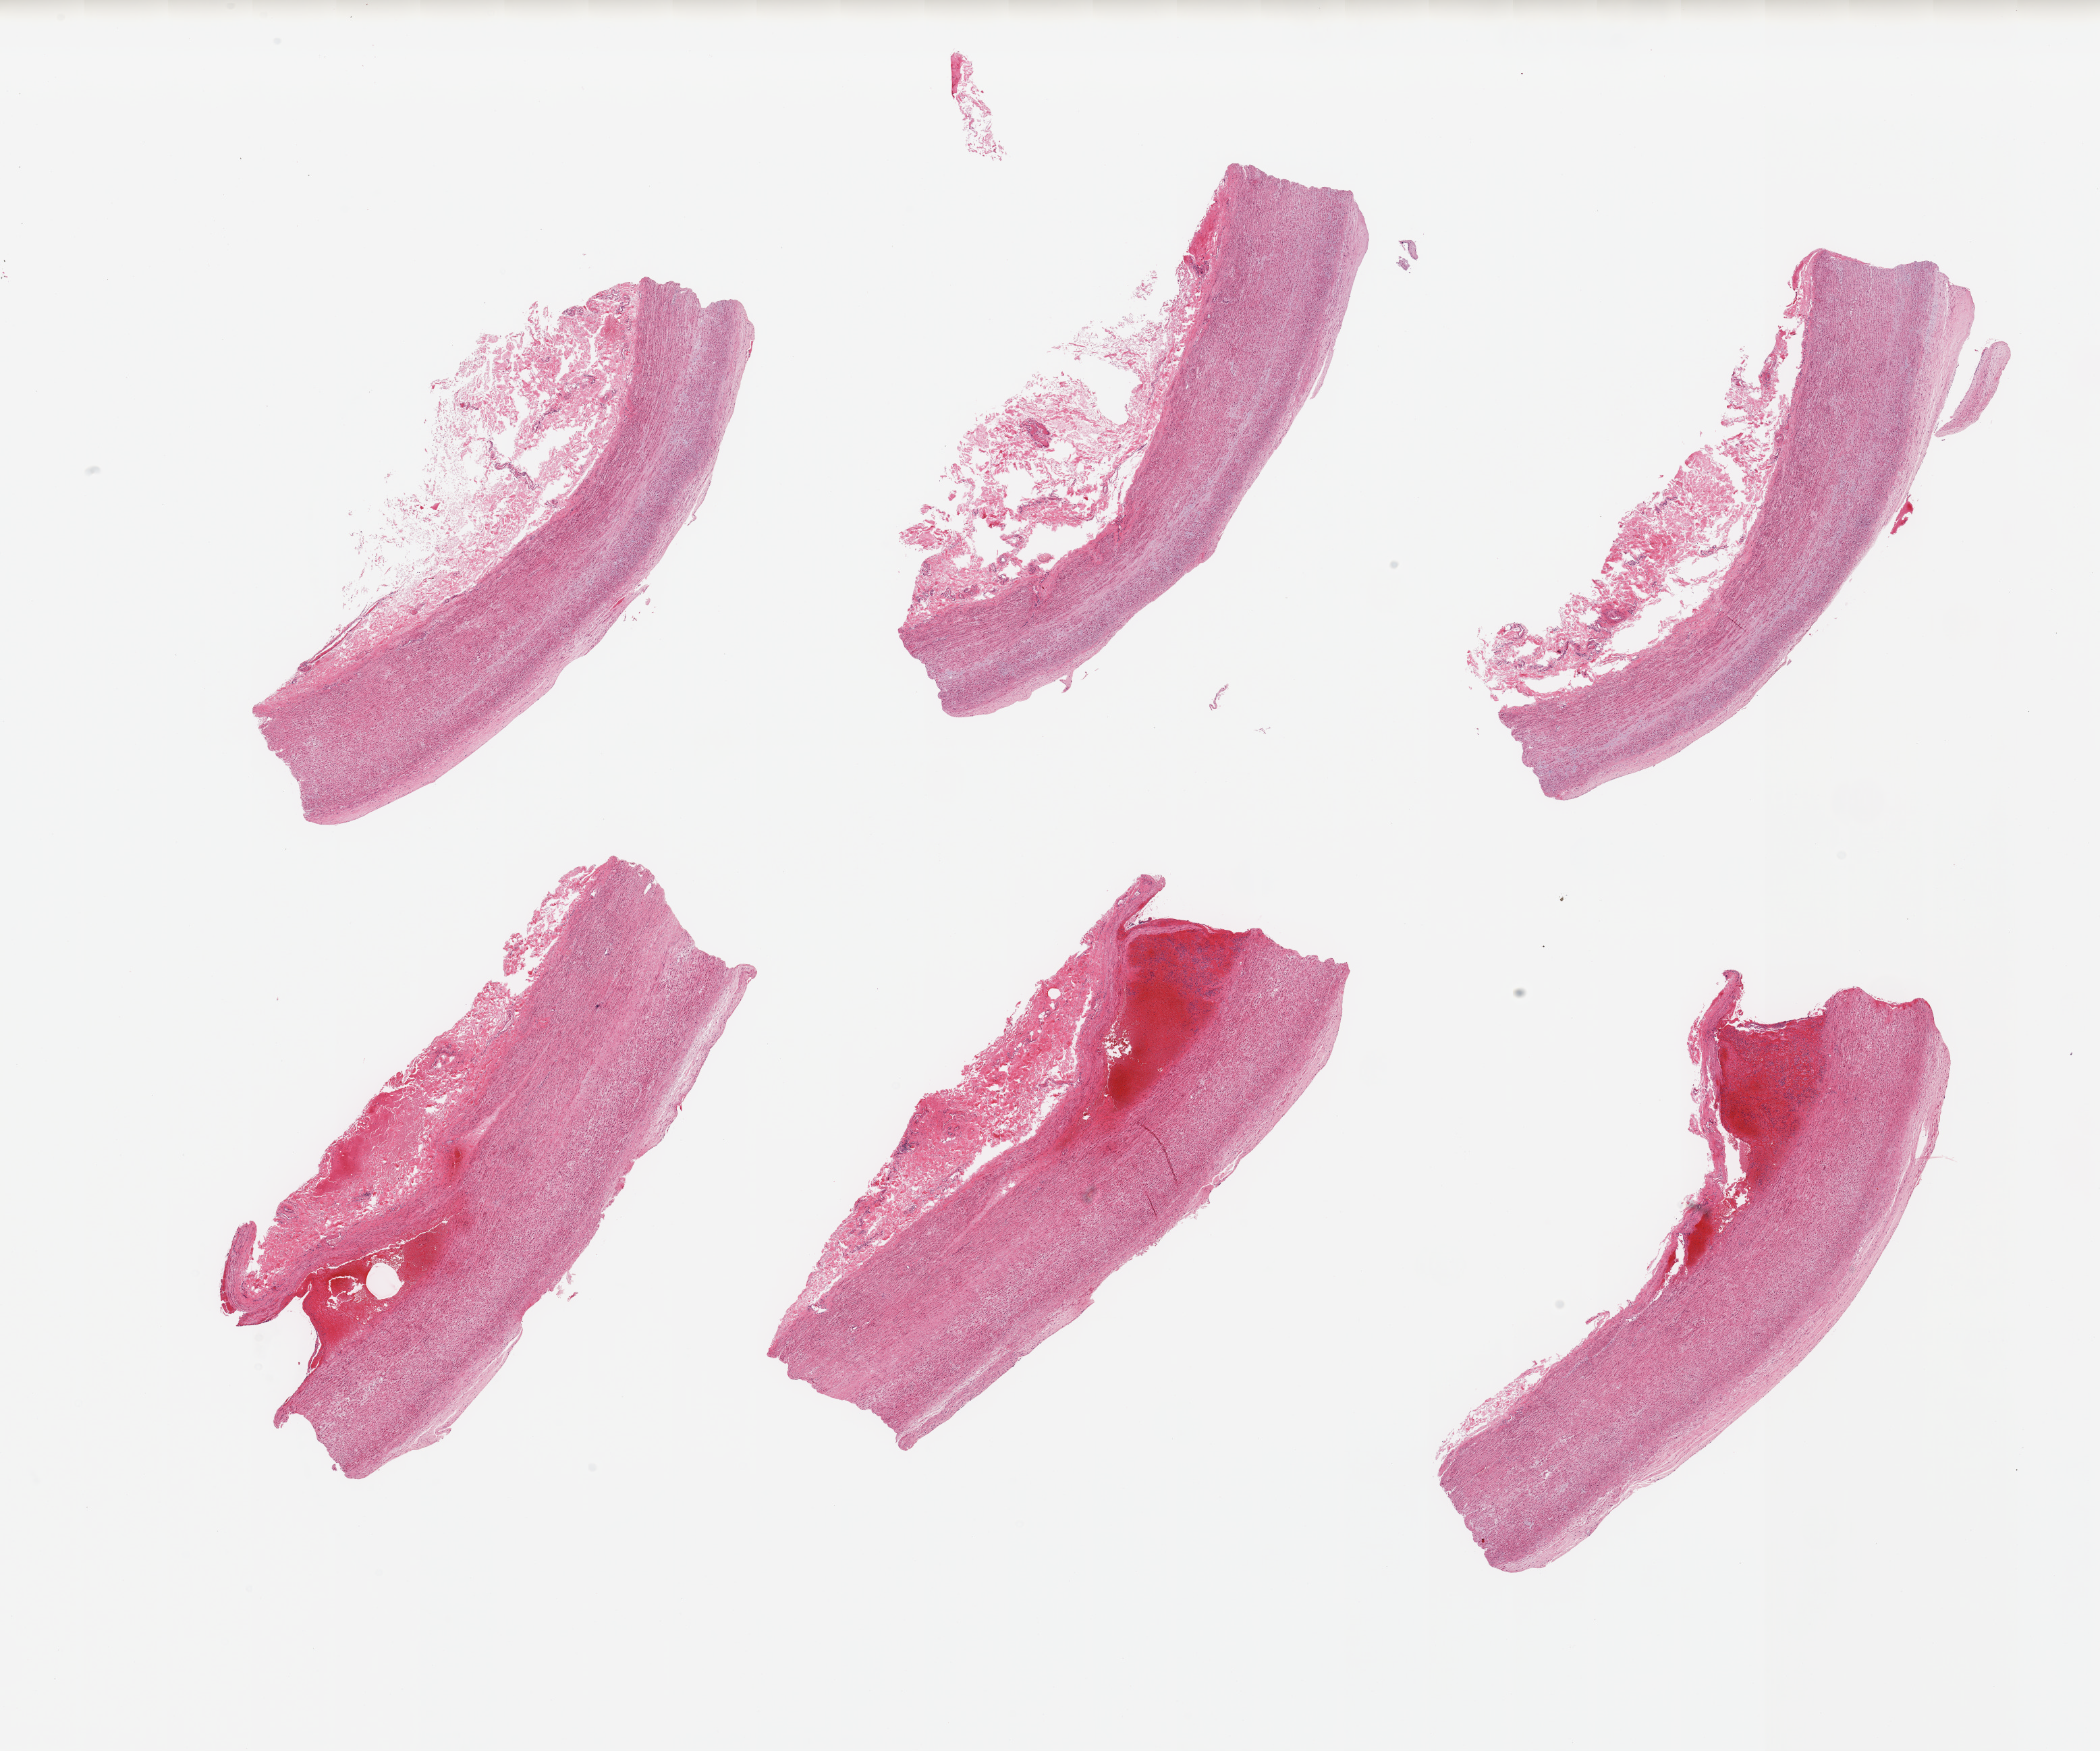
Digitized H&E-stained section, shown as a low-resolution overview of the whole scanned area (about 24.6 x 20.5 mm). PAXgene-fixed paraffin-embedded (PFPE) section. Target tissue: aorta. Tissue donor sample. Donor sex: male.
Review note (as recorded): 6 pieces; aortic dissection in 3 of 6 pieces.